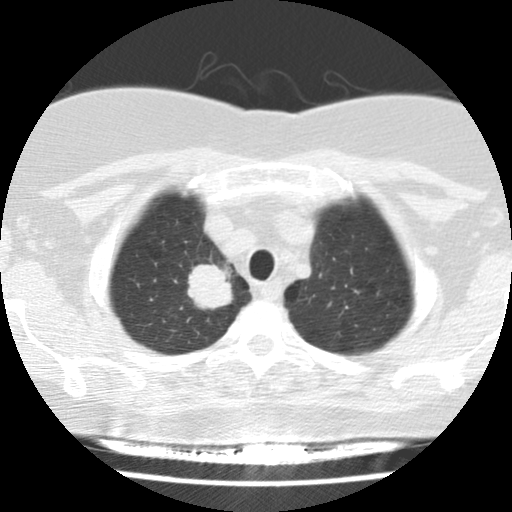
Low-dose screening chest CT, one axial slice. Slice 129 of 148 in the series (ordered by position). Reconstruction kernel STANDARD. Lung window (W 1500 / L -600 HU). 2.5 mm slice thickness. 512 × 512 image matrix.
Outlined on this slice (manually delineated by an expert):
- lesion 1 (tumor, upper lobe of right lung): bounding box <187,264,233,310> (left, top, right, bottom; pixels)